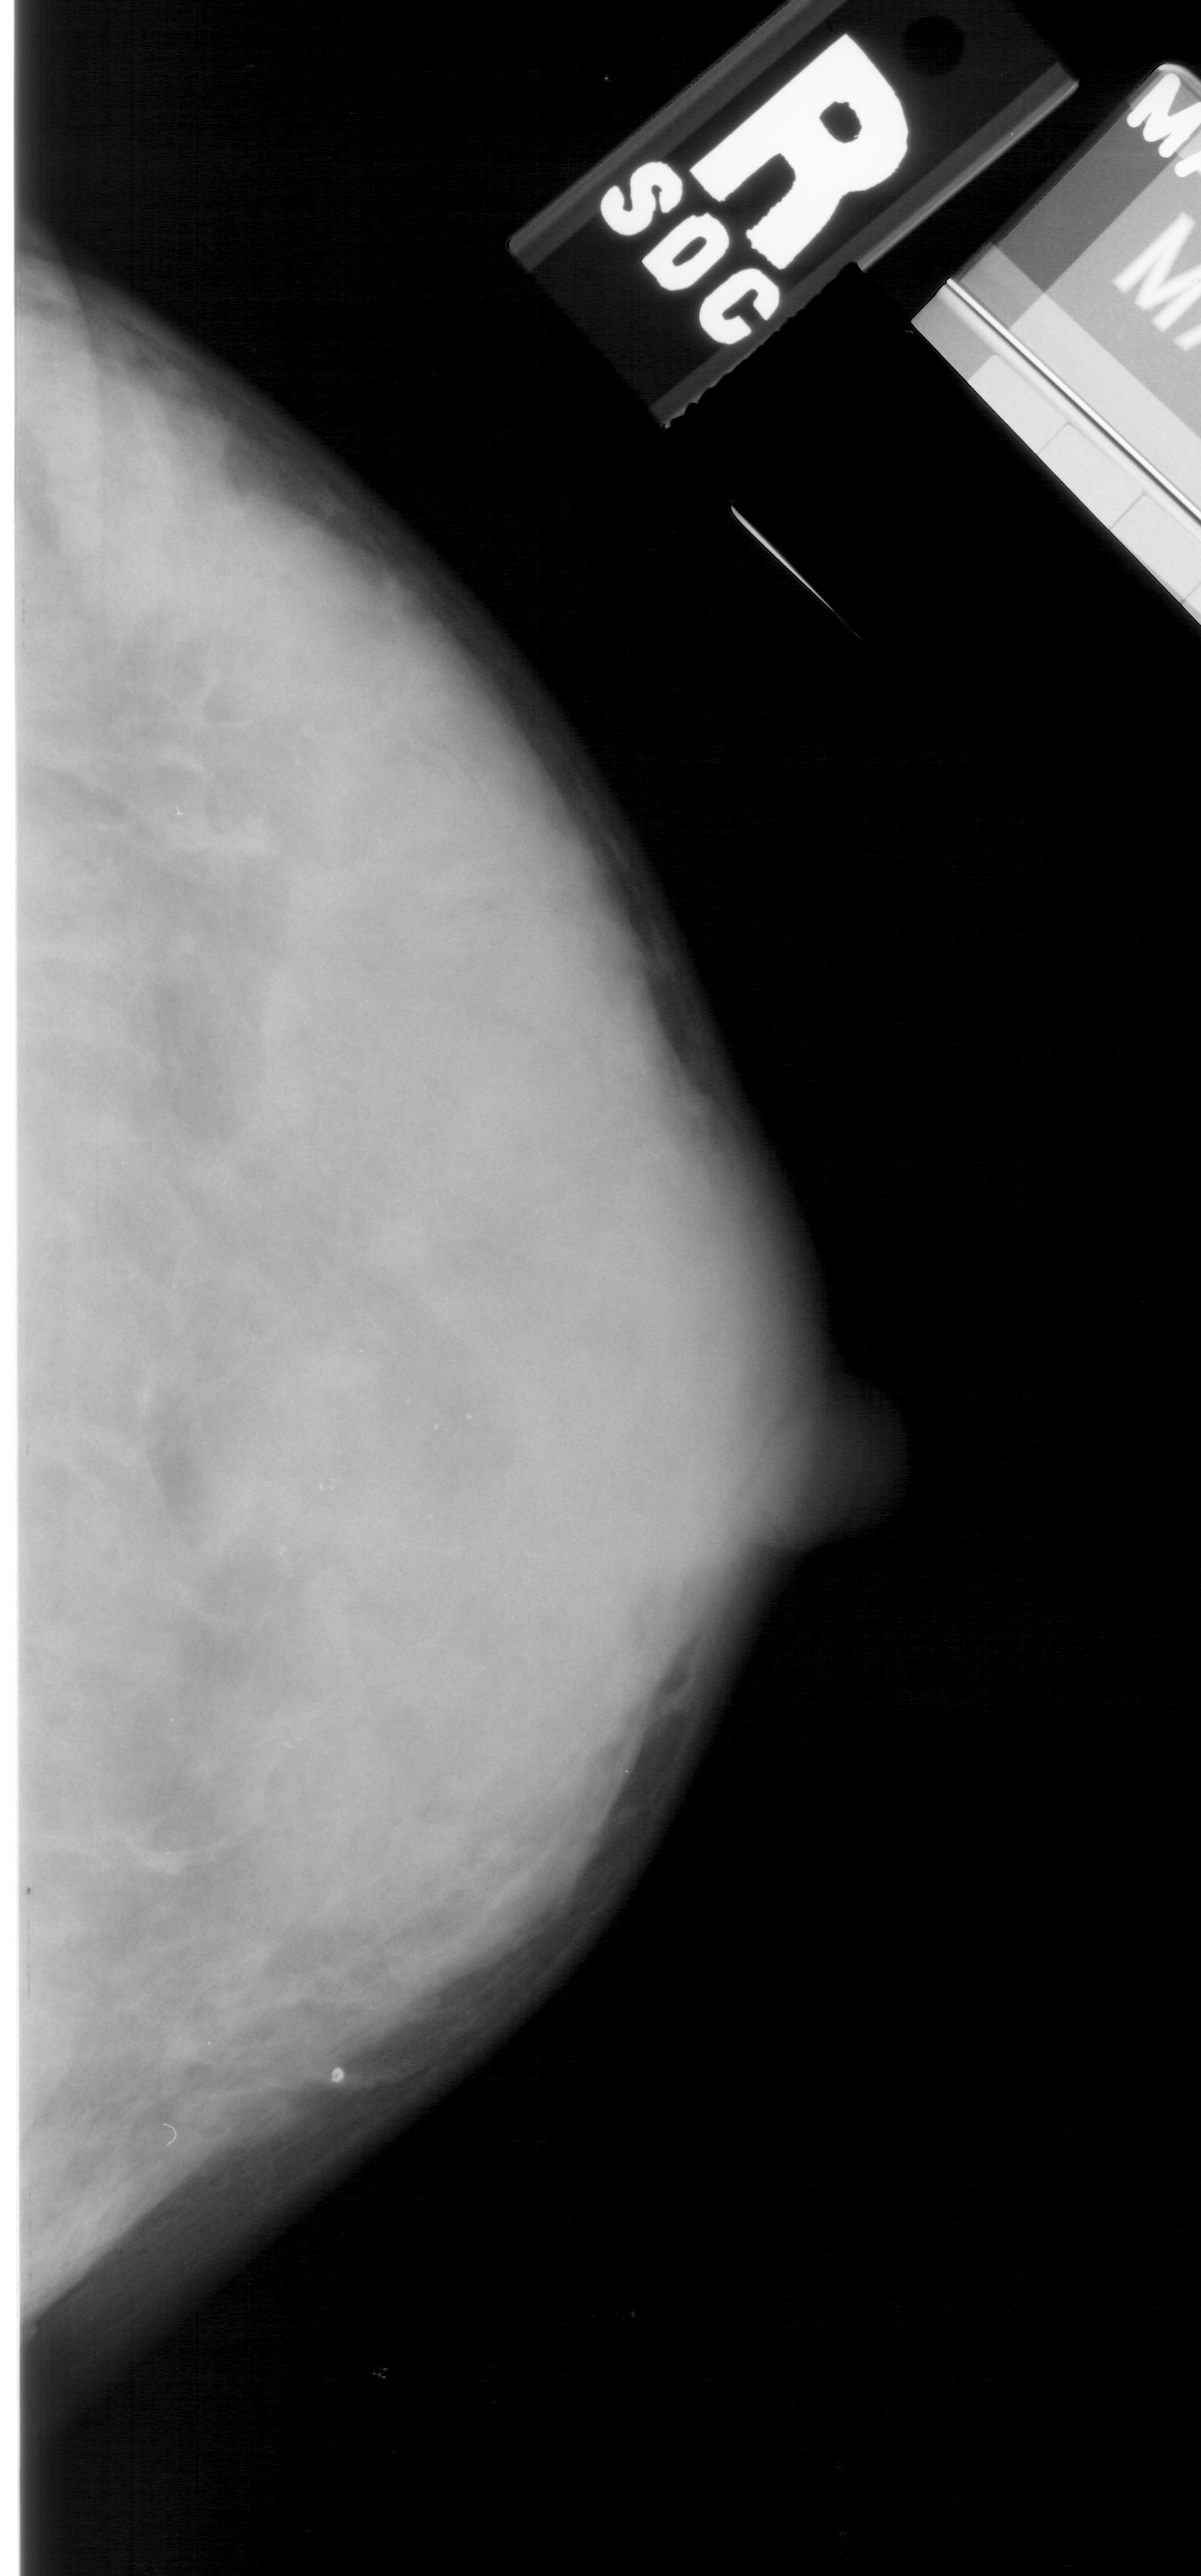
Digitized screen-film mammogram, right breast, CC view.
Marked findings (only marked abnormalities are described; nothing is implied about the rest of the image): calcifications, morphology pleomorphic, distribution segmental; BI-RADS assessment category 4; pathology (as recorded): benign.